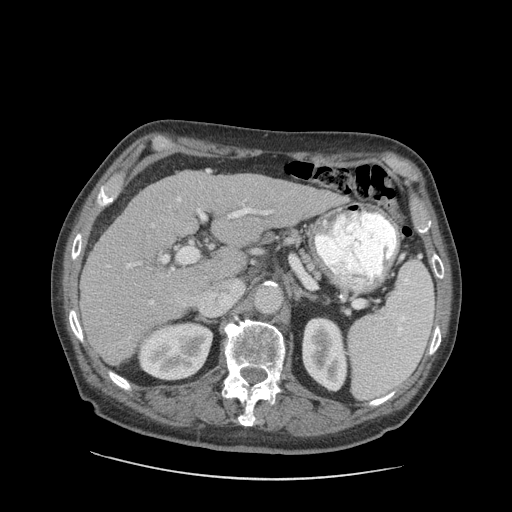
Contrast-enhanced abdominal CT (liver protocol), one axial slice. Position 52 of 89 along the scan axis. Soft-tissue window (W 400 / L 40 HU). 2.5 mm slice thickness. 512 × 512 image matrix, field of view 420 × 420 mm. From the clinical record (not read from this slice): diagnosis: hepatocellular carcinoma (patient treated with transarterial chemoembolisation; whether this scan precedes or follows treatment is not stated here); TNM stage (as recorded): Stage-I; Child-Pugh class: A; tumour nodularity: uninodular.
Outlined on this slice (semi-automatic segmentation, software-assisted and operator-edited):
- liver parenchyma outside the tumour (the mass and vessels are separate outlines, so this box may not span the whole liver): box from (x=80, y=170) to (x=340, y=366) px
- liver vessels: (x=102, y=171)–(x=273, y=340)